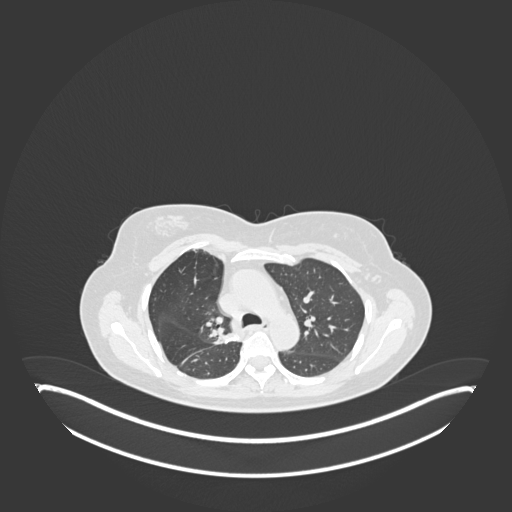
Chest CT, one axial slice; slice 117 of 181 in the series (ordered by position); lung window (W 1500 / L -600 HU); 512 × 512 image matrix. Female patient, age 65 years. Case-level facts recorded for this patient, not image findings: clinical TNM (as recorded): T1b N0 M0; histopathological grade: G2.
Structures marked on this image (bounding box drawn by a radiologist):
- lung tumour (recorded histology: adenocarcinoma): bounding box [x1, y1, x2, y2] px = [211, 329, 238, 351]